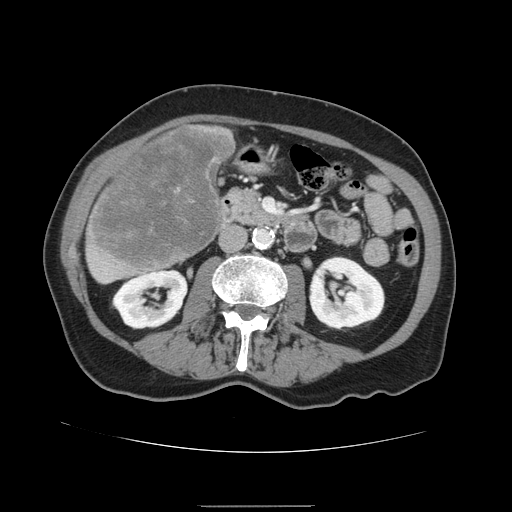
Contrast-enhanced abdominal CT, one axial slice; slice 46 of 168 in the series (ordered by position); 120 kVp; intravenous contrast given; soft-tissue window (W 400 / L 40 HU); 512 × 512 image matrix, field of view 386 × 386 mm. Male patient, age 74 years. From the clinical record (not read from this slice): diagnosis: colorectal cancer liver metastases, imaged before liver resection; multiple liver metastases: no; largest metastasis: 14.5 cm; disease in both lobes: yes.
Structures marked on this image (manually delineated by an expert):
- liver: box from (x=84, y=123) to (x=236, y=284) px
- liver metastasis: (x=90, y=127)–(x=233, y=270)